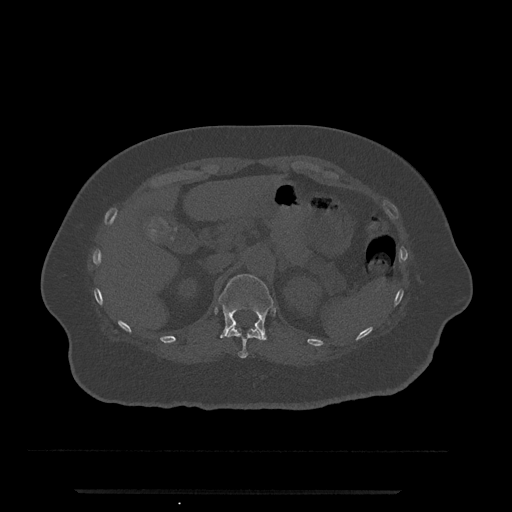
CT including the spine, one axial slice; slice 192 of 797 in the series (ordered by position); reconstruction kernel Br40s/3; 120 kVp; bone window (W 1800 / L 400 HU); 0.5 mm slice thickness; 512 × 512 image matrix. Patient: female, 51 years. Case-level facts recorded for this patient, not image findings: primary cancer: neuro.
Structures marked on this image (semi-automatically segmented with operator editing):
- T11 vertebra: box from (x=226, y=327) to (x=261, y=359) px
- T12 vertebra: (x=218, y=274)–(x=274, y=341)